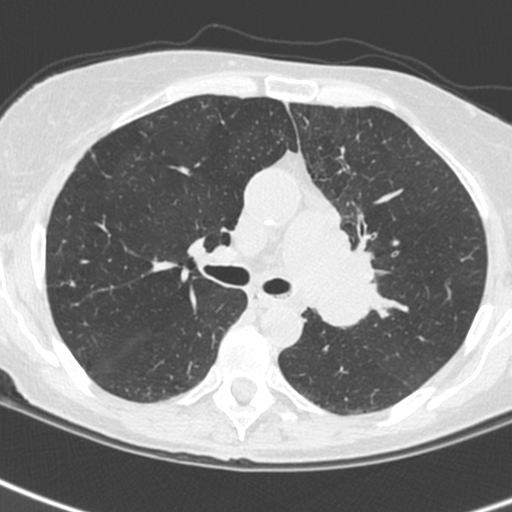
Low-dose screening chest CT, one axial slice; position 156 of 242 along the scan axis; 120 kVp; lung window (W 1500 / L -600 HU); 1.3 mm slice thickness; 512 × 512 image matrix, field of view 284 × 284 mm.
Outlined on this slice (expert manual segmentation):
- lesion 3 (tumor, upper lobe of left lung): bounding box <312,203,378,328> (left, top, right, bottom; pixels)